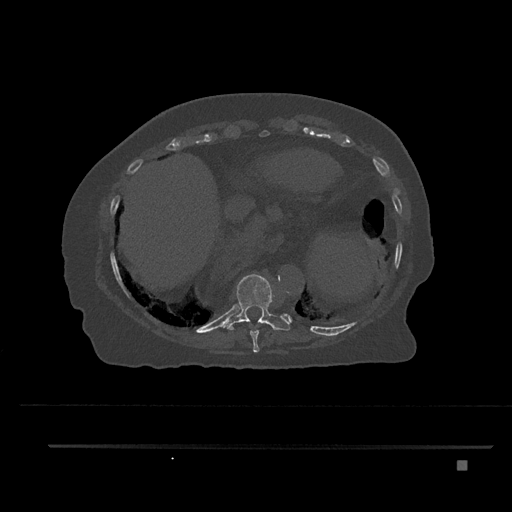
CT including the spine, one axial slice; reconstruction kernel Br40s/3; bone window (W 1800 / L 400 HU); 512 × 512 image matrix, field of view 437 × 437 mm. Female patient, age 76 years. From the clinical record (not read from this slice): primary cancer: lung; vertebrae with lytic lesions (as recorded): T11, L3.
Structures marked on this image (semi-automatically segmented with operator editing):
- T10 vertebra: box from (x=220, y=274) to (x=290, y=331) px
- T9 vertebra: (x=250, y=320)–(x=259, y=352)